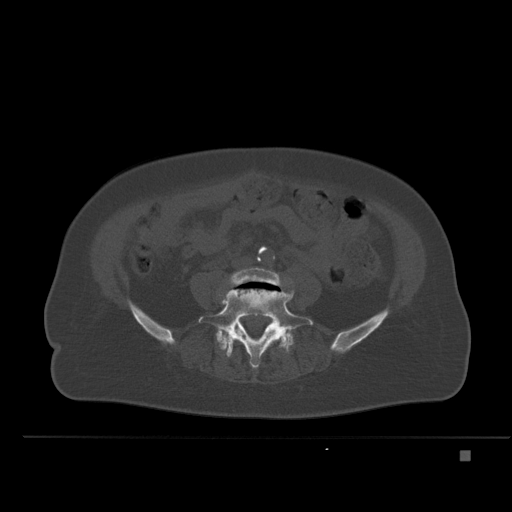
CT including the spine, one axial slice; position 165 of 477 along the scan axis; bone window (W 1800 / L 400 HU); 1.5 mm slice thickness; 512 × 512 image matrix. Female patient, age 74 years. From the clinical record (not read from this slice): primary cancer: colon.
Structures marked on this image (semi-automatic segmentation, software-assisted and operator-edited):
- L4 vertebra: box from (x=229, y=268) to (x=282, y=287) px
- L5 vertebra: (x=198, y=290)–(x=313, y=369)